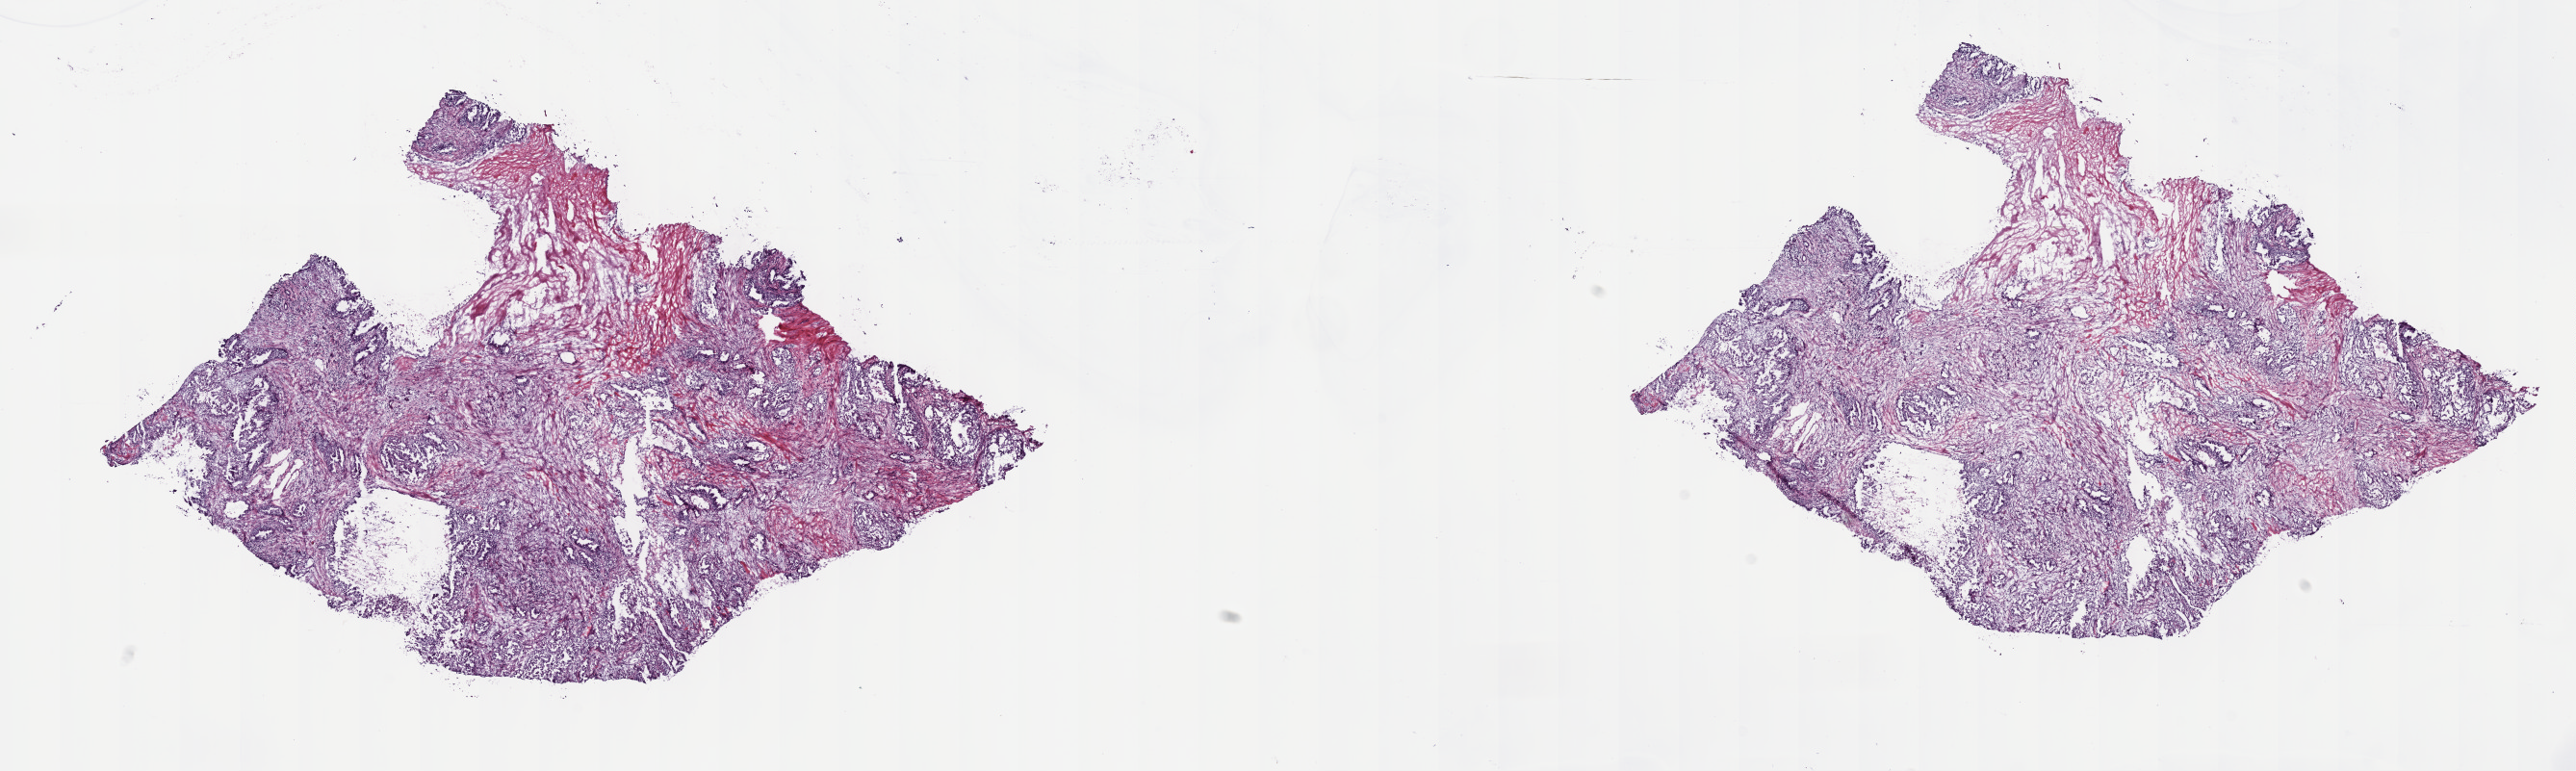
Whole-slide histology image, H&E-stained — low-resolution overview of the scanned area, about 21.6 x 6.5 mm (from a 40x scan); frozen section from the top of the tissue portion; sample: primary tumour, pancreas. Male patient; age at initial diagnosis 76 years. Histologic grade: G2 (moderately differentiated). Composition of this section per pathologist review: tumour cells 100%, tumour nuclei 65%, normal cells 0%, stromal cells 0%, necrosis 0%. Infiltration values recorded for this section: lymphocyte infiltration 5%, monocyte infiltration 0%, neutrophil infiltration 0%.
• diagnosis: Infiltrating duct carcinoma, NOS
• AJCC pathologic stage: IIB (7th edition)